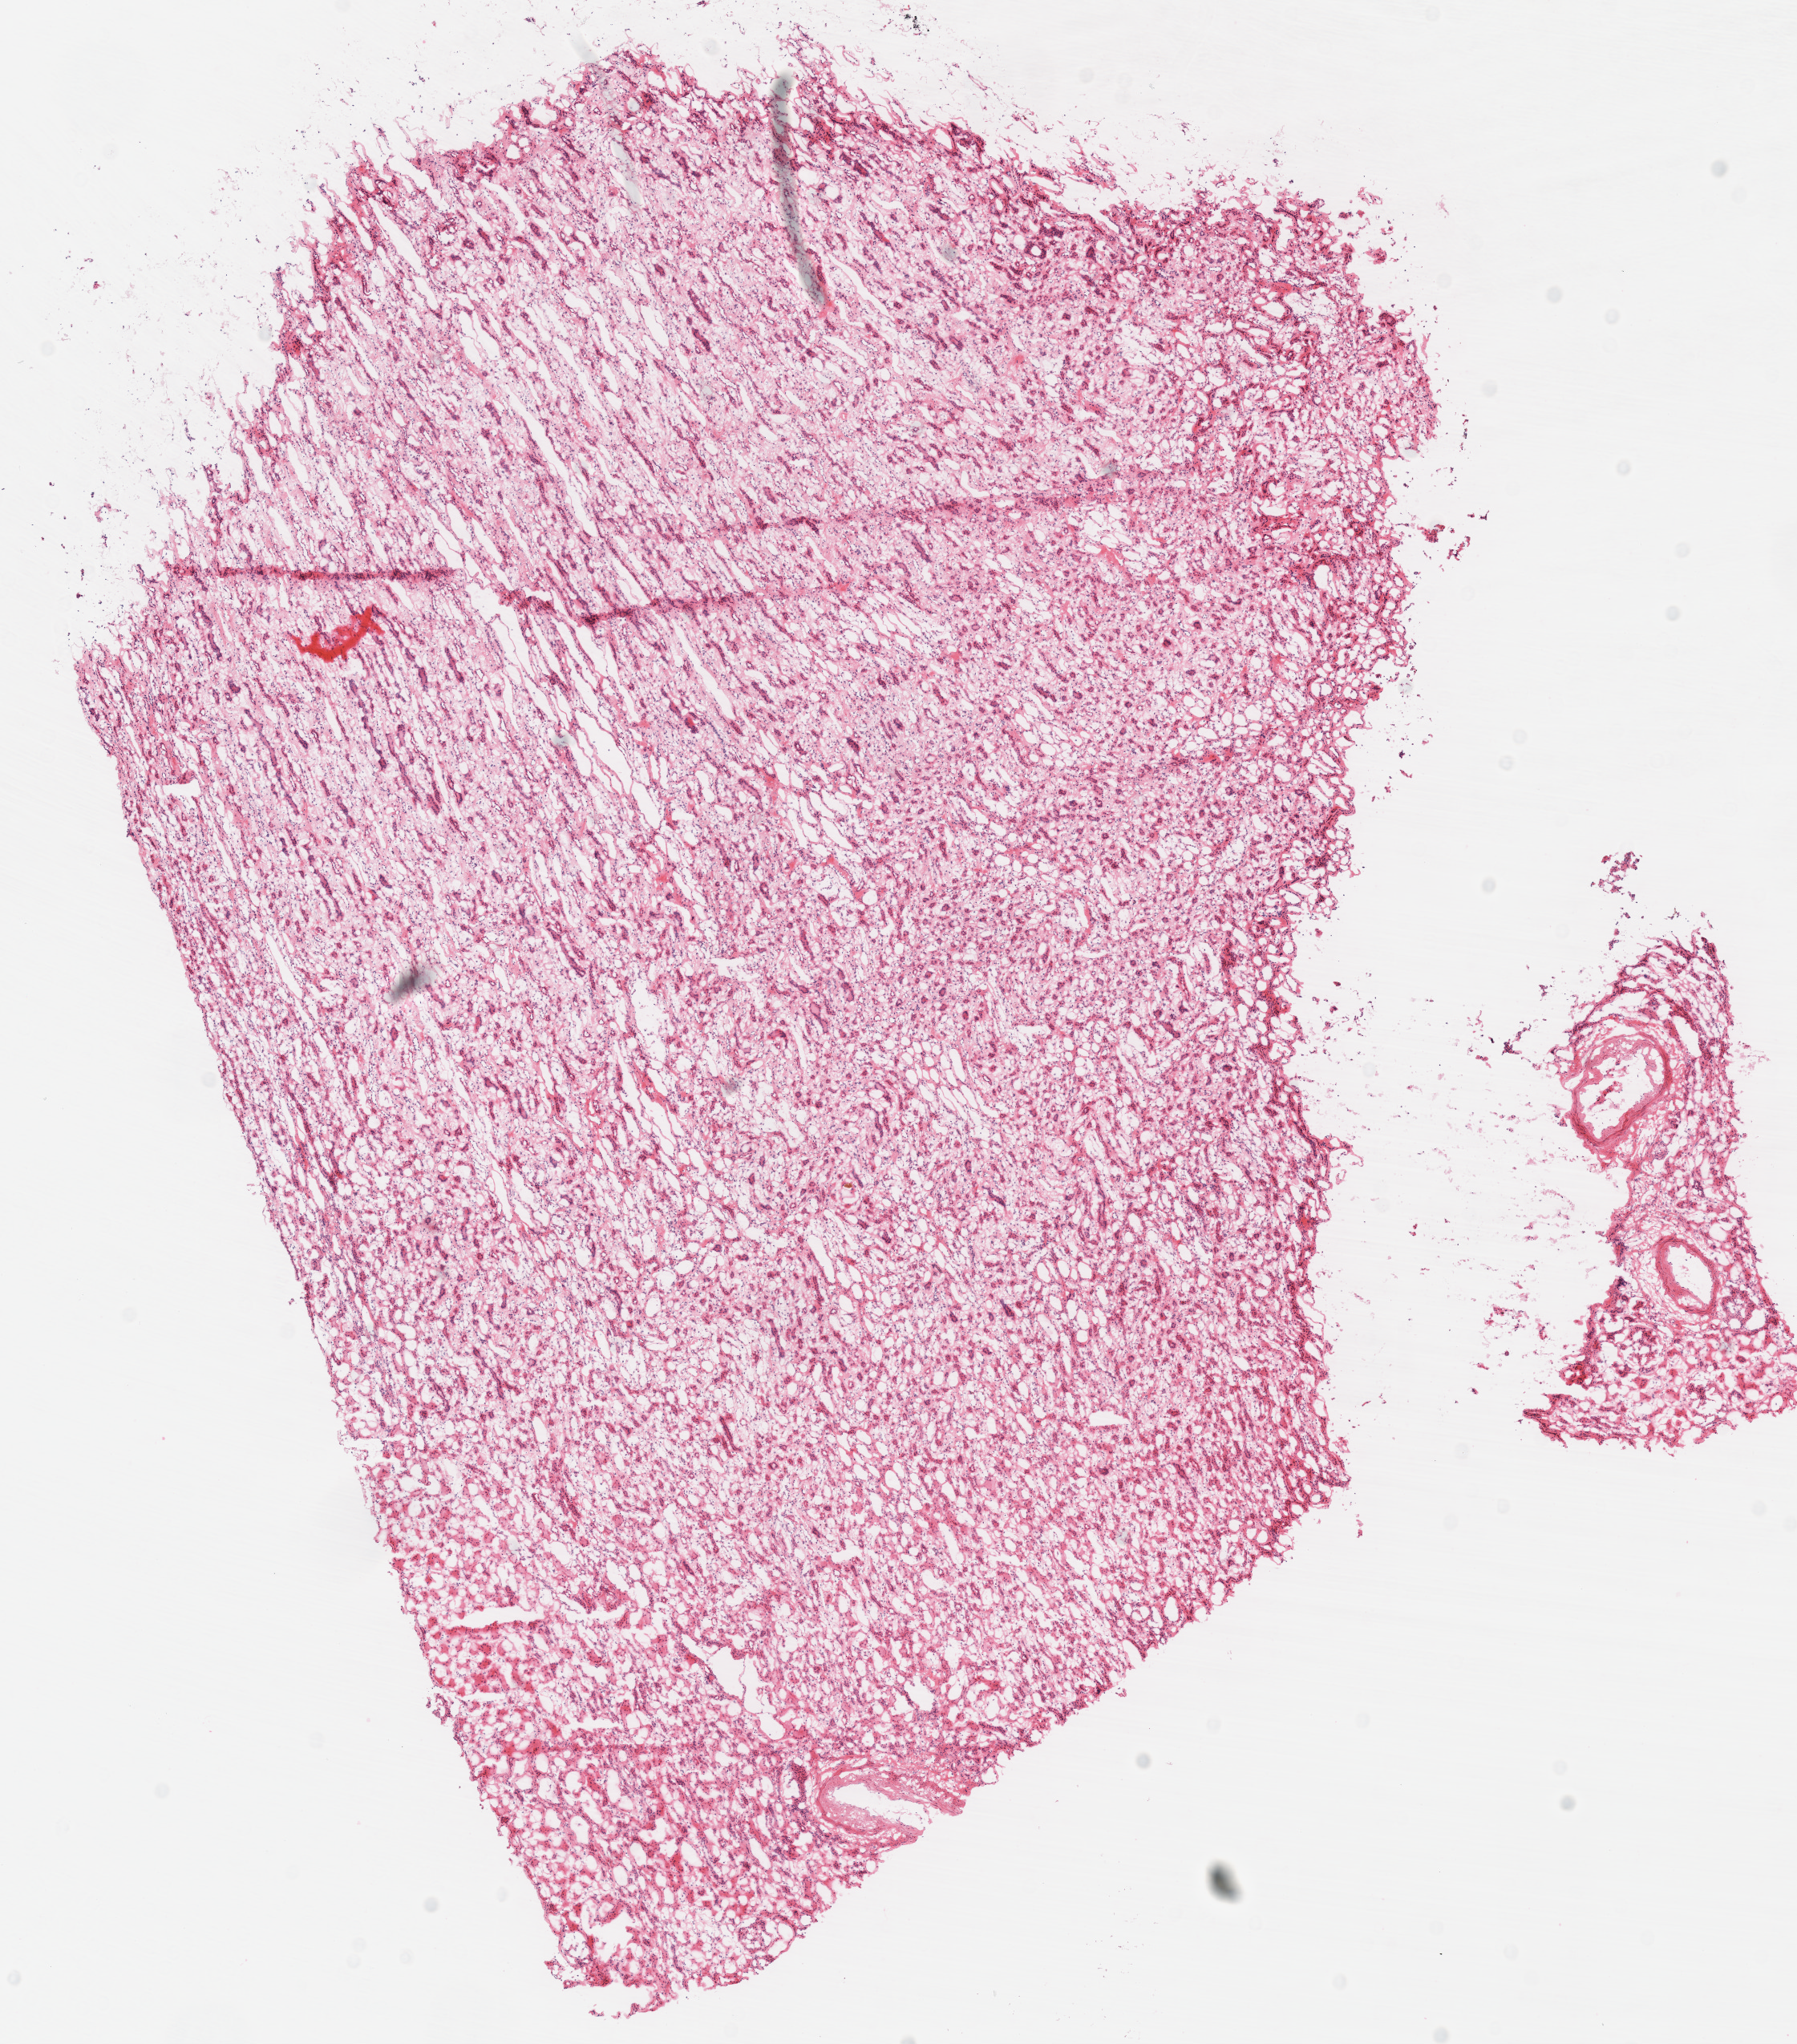
Whole-slide histology image, H&E, low-resolution overview of the scanned area, about 8.8 x 10.0 mm (slide scanned at 40x); frozen section from the top of the tissue portion; solid tissue normal (non-tumour tissue) sample from the kidney. Patient: female, age at initial diagnosis 46 years.
This section: solid tissue normal (non-tumour) sample from the same patient. Patient diagnosis: Renal cell carcinoma, chromophobe type.